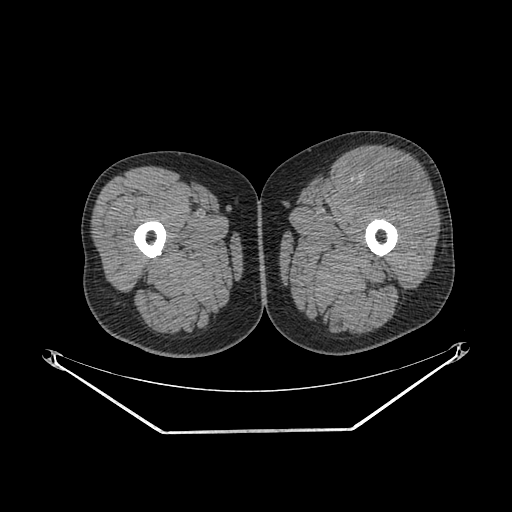
CT of an extremity soft-tissue mass (from a PET/CT study), one axial slice. Slice 236 of 267 in the series (ordered by position). Reconstruction kernel SOFT. Soft-tissue window (W 400 / L 40 HU). 3.75 mm slice thickness. 512 × 512 image matrix, field of view 500 × 500 mm. Male patient. From the clinical record (not read from this slice): histological type: extraskeletal osteosarcoma; grade: high; site of the primary tumour: thigh.
Structures marked on this image (expert contour drawn on MRI and transferred to this co-registered scan by the dataset authors):
- gross tumour volume (mass): box from (x=352, y=158) to (x=430, y=211) px